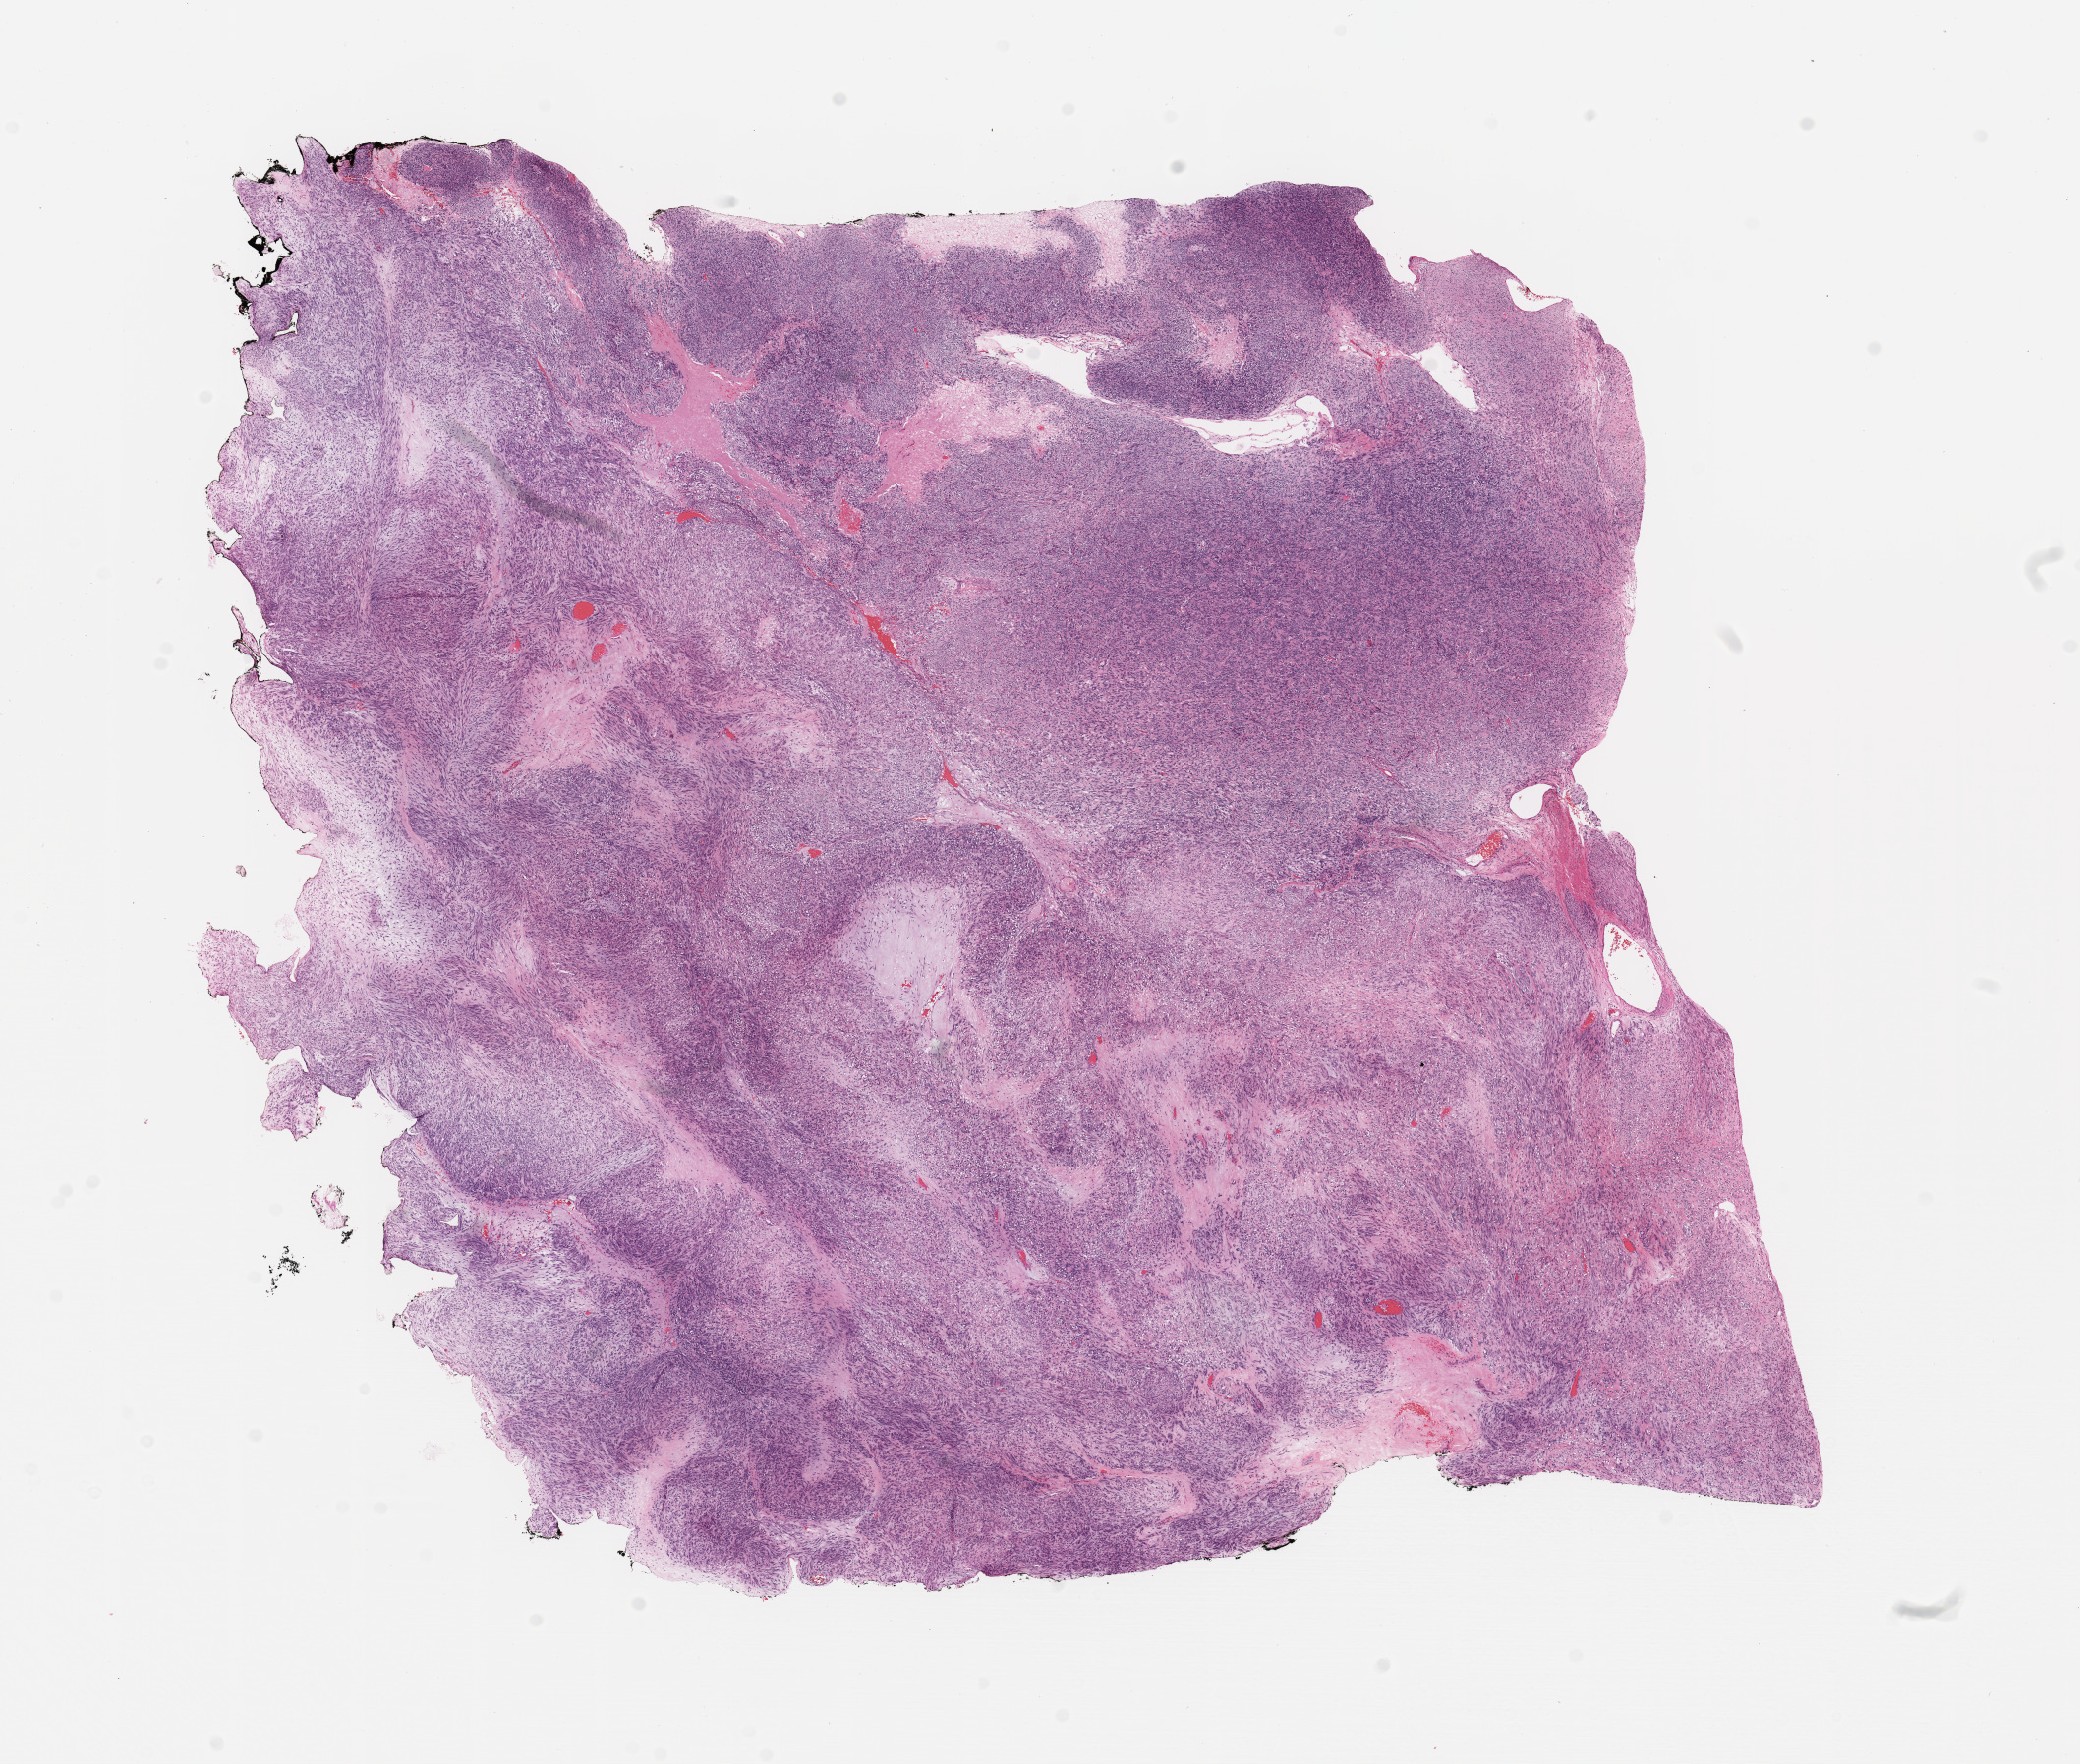
Whole-slide histology image, H&E-stained — shown as a low-resolution overview of the whole scanned area (about 16.7 x 14.2 mm, acquisition: 20x scan). Patient: female, age 65 years.
• patient diagnosis (cohort enrolment): sarcoma (site not recorded at cohort level)